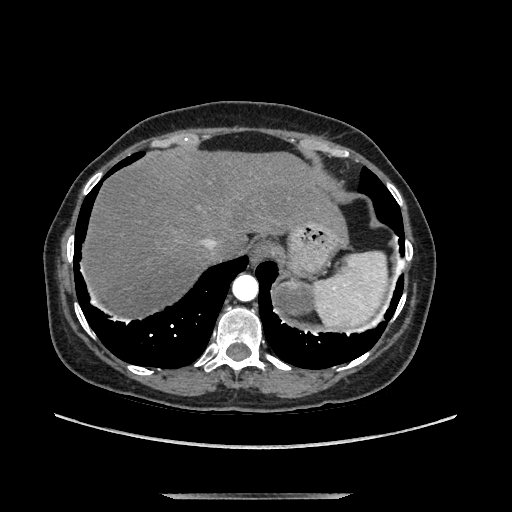
Contrast-enhanced abdominal CT, one axial slice; position 118 of 169 along the scan axis; soft-tissue window (W 400 / L 40 HU); 512 × 512 image matrix, field of view 400 × 400 mm. Female patient. Case-level facts recorded for this patient, not image findings: diagnosis: adrenocortical carcinoma; tumour side: left adrenal; tumour size at pathology: 9 cm; Ki-67 index: 2 %; stage (as recorded): 3.
Structures marked on this image (semi-automatic segmentation, software-assisted and operator-edited):
- mass: bounding box [x1, y1, x2, y2] px = [278, 283, 312, 314]